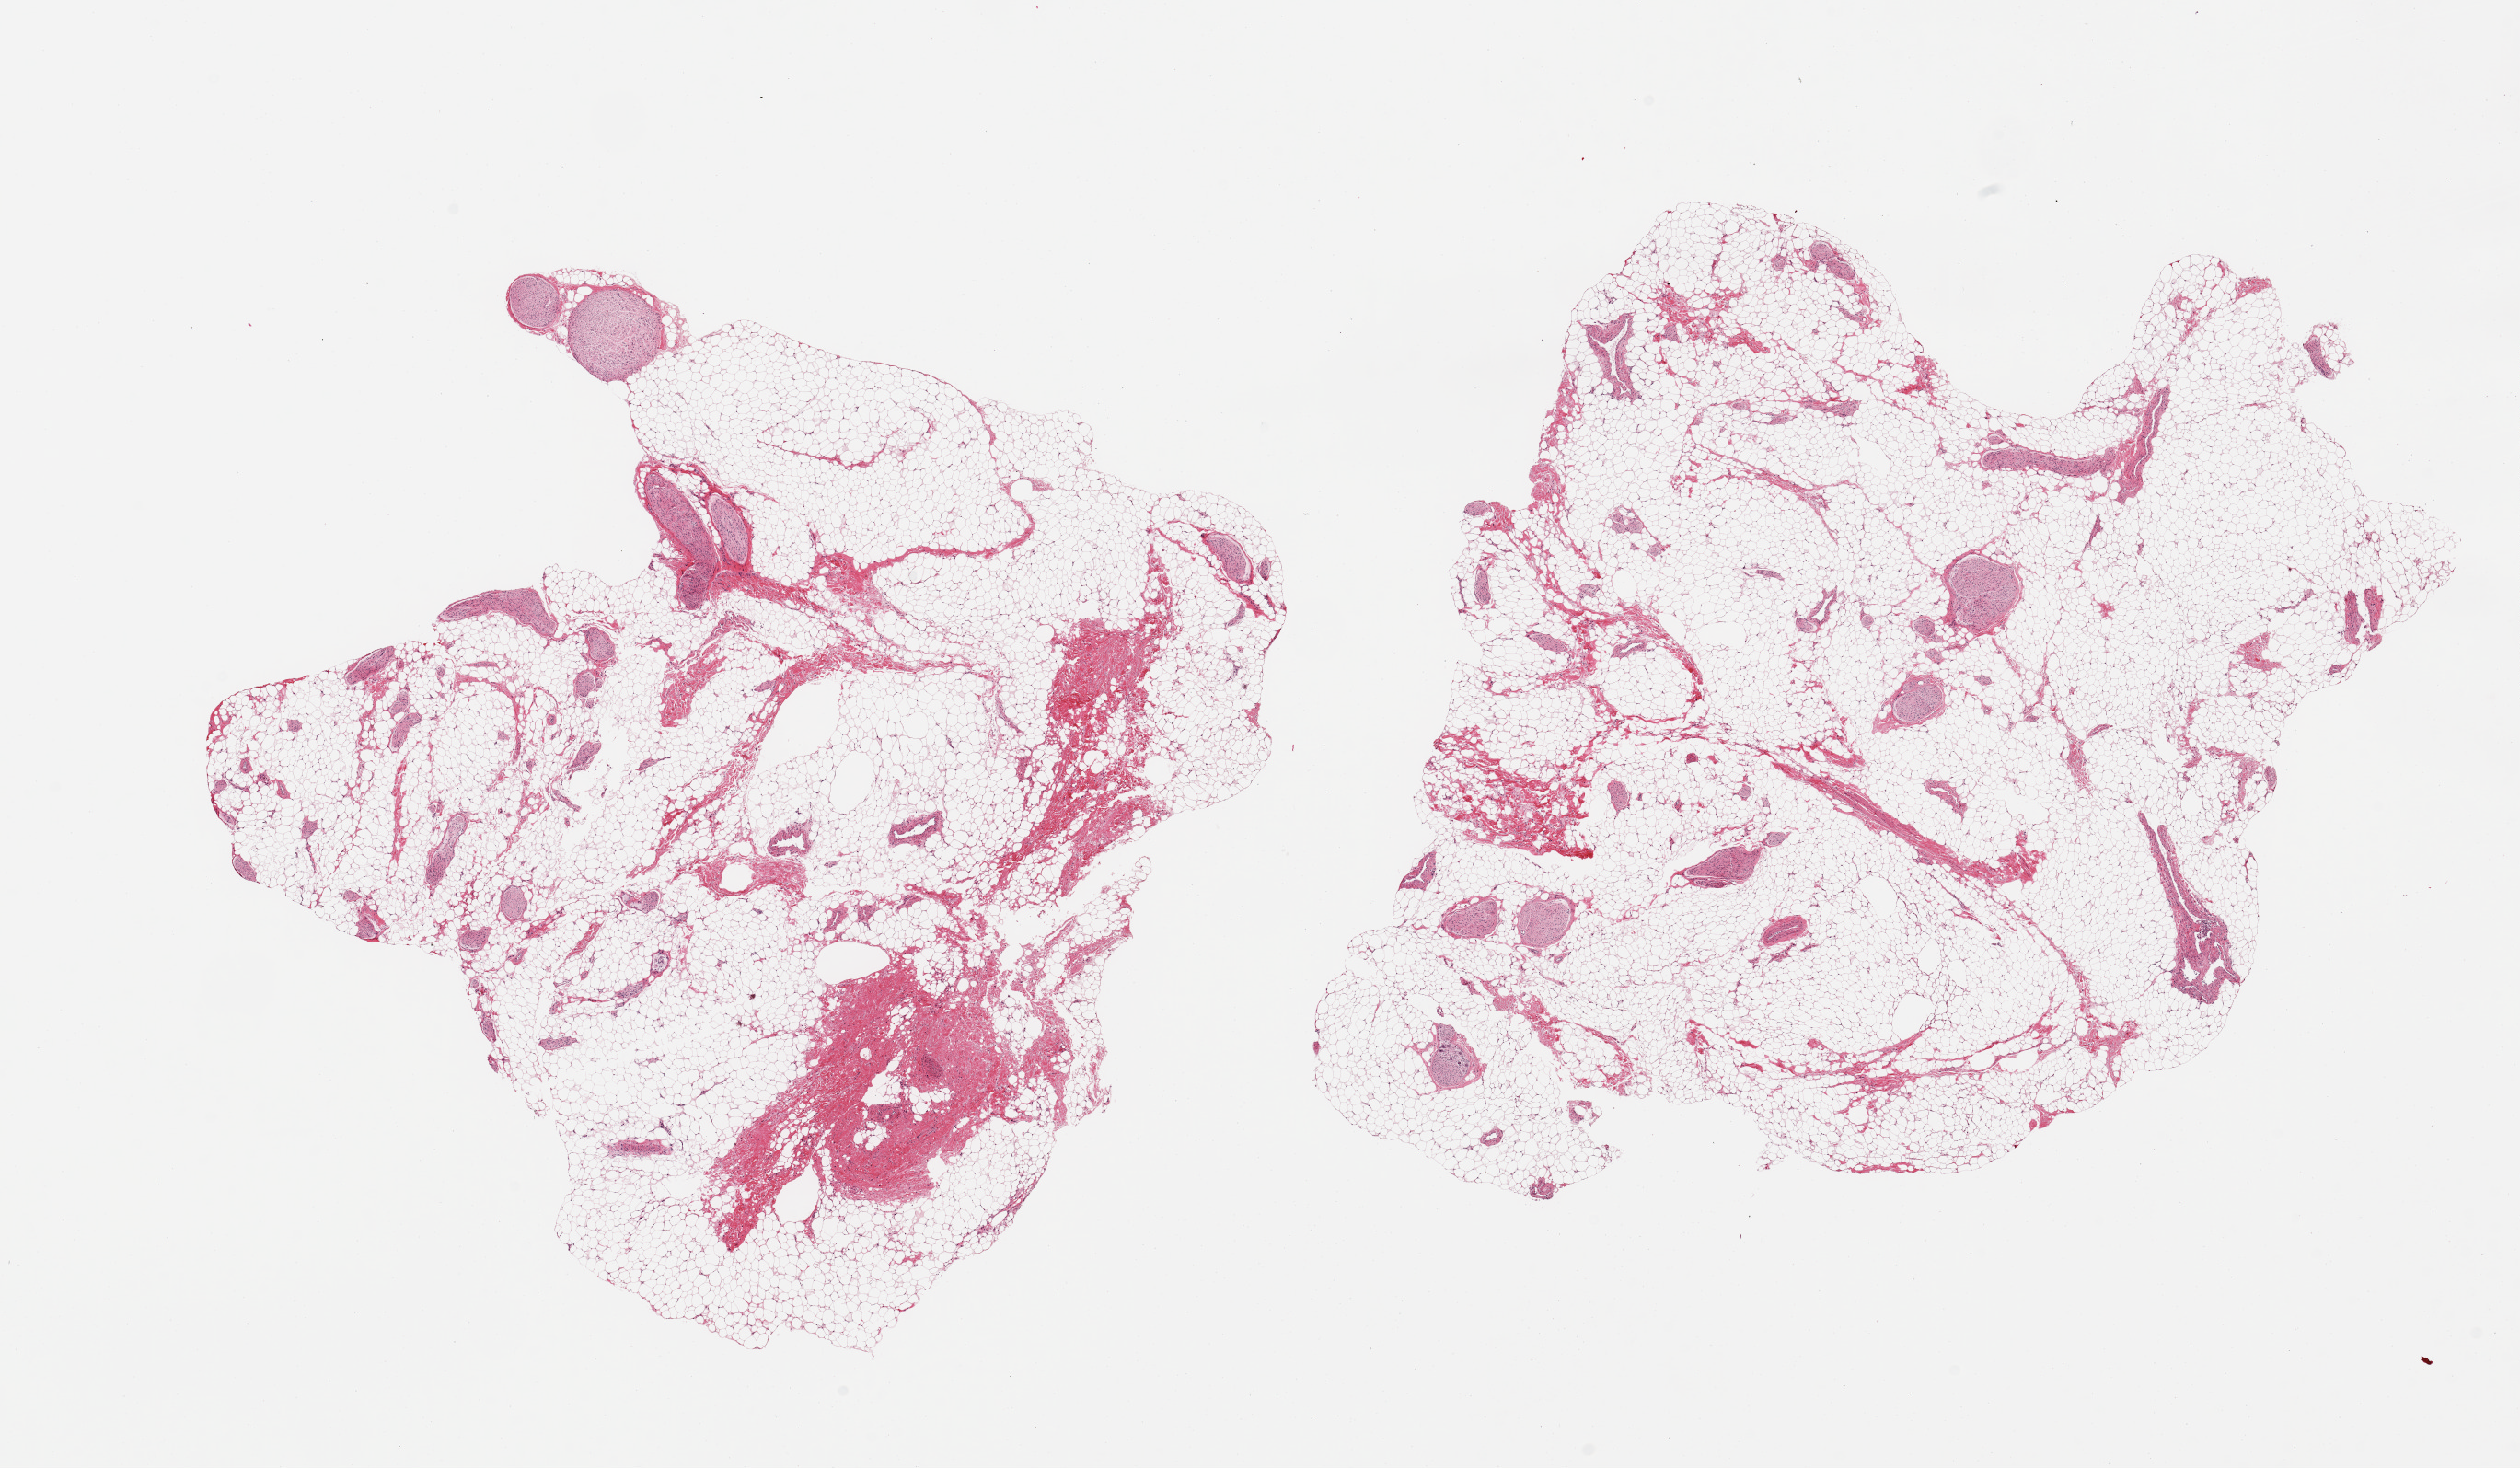
Digitized haematoxylin and eosin-stained section — low-resolution overview of the scanned area, about 21.7 x 12.6 mm. PAXgene-fixed paraffin-embedded (PFPE) section. Section of pancreas (target tissue). Donor tissue sample.
* pathologist's review note for this sample: 2 pieces; adipose tissue with 10% fibrous stroma and nerve; no pancreatic tissue